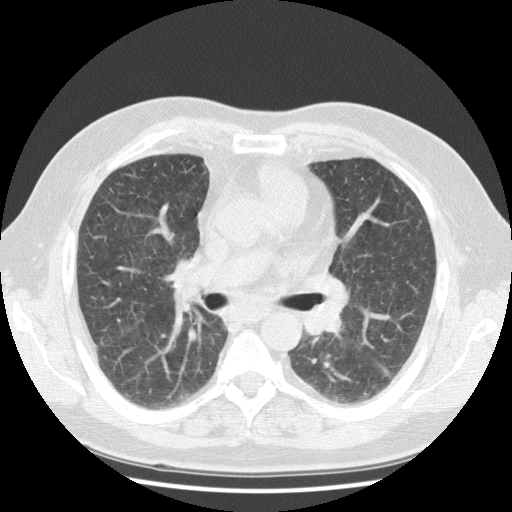
Low-dose screening chest CT, one axial slice; position 65 of 108 along the scan axis; lung window (W 1500 / L -600 HU); 2.5 mm slice thickness; 512 × 512 image matrix, field of view 350 × 350 mm.
Annotated regions visible in this slice (manually delineated by an expert):
- lesion 1 (tumor, hilum of left lung): bounding box (x1, y1, x2, y2) in pixels: (305, 293, 347, 335)